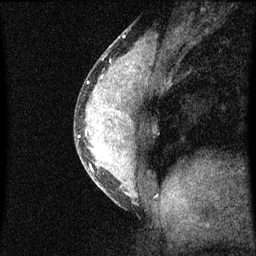
Breast MRI (dynamic contrast-enhanced), one sagittal slice; position 24 of 60 along the scan axis; dynamic contrast-enhanced series, image 2 of 3 at this slice position (ordered by acquisition); 1.5 T; TE 4.2 ms, TR 8 ms; 256 × 256 image matrix, field of view 180 × 180 mm. Female patient, age 33 years.
Structures marked on this image (semi-automatically segmented with operator editing):
- analysis volume of interest (the breast-tissue region the enhancement analysis was run in; not a lesion): bounding box [x1, y1, x2, y2] px = [74, 56, 154, 209]
- tumour enhancement mask (voxels above the 70 % enhancement threshold inside the analysis volume of interest): [79, 60, 136, 195]